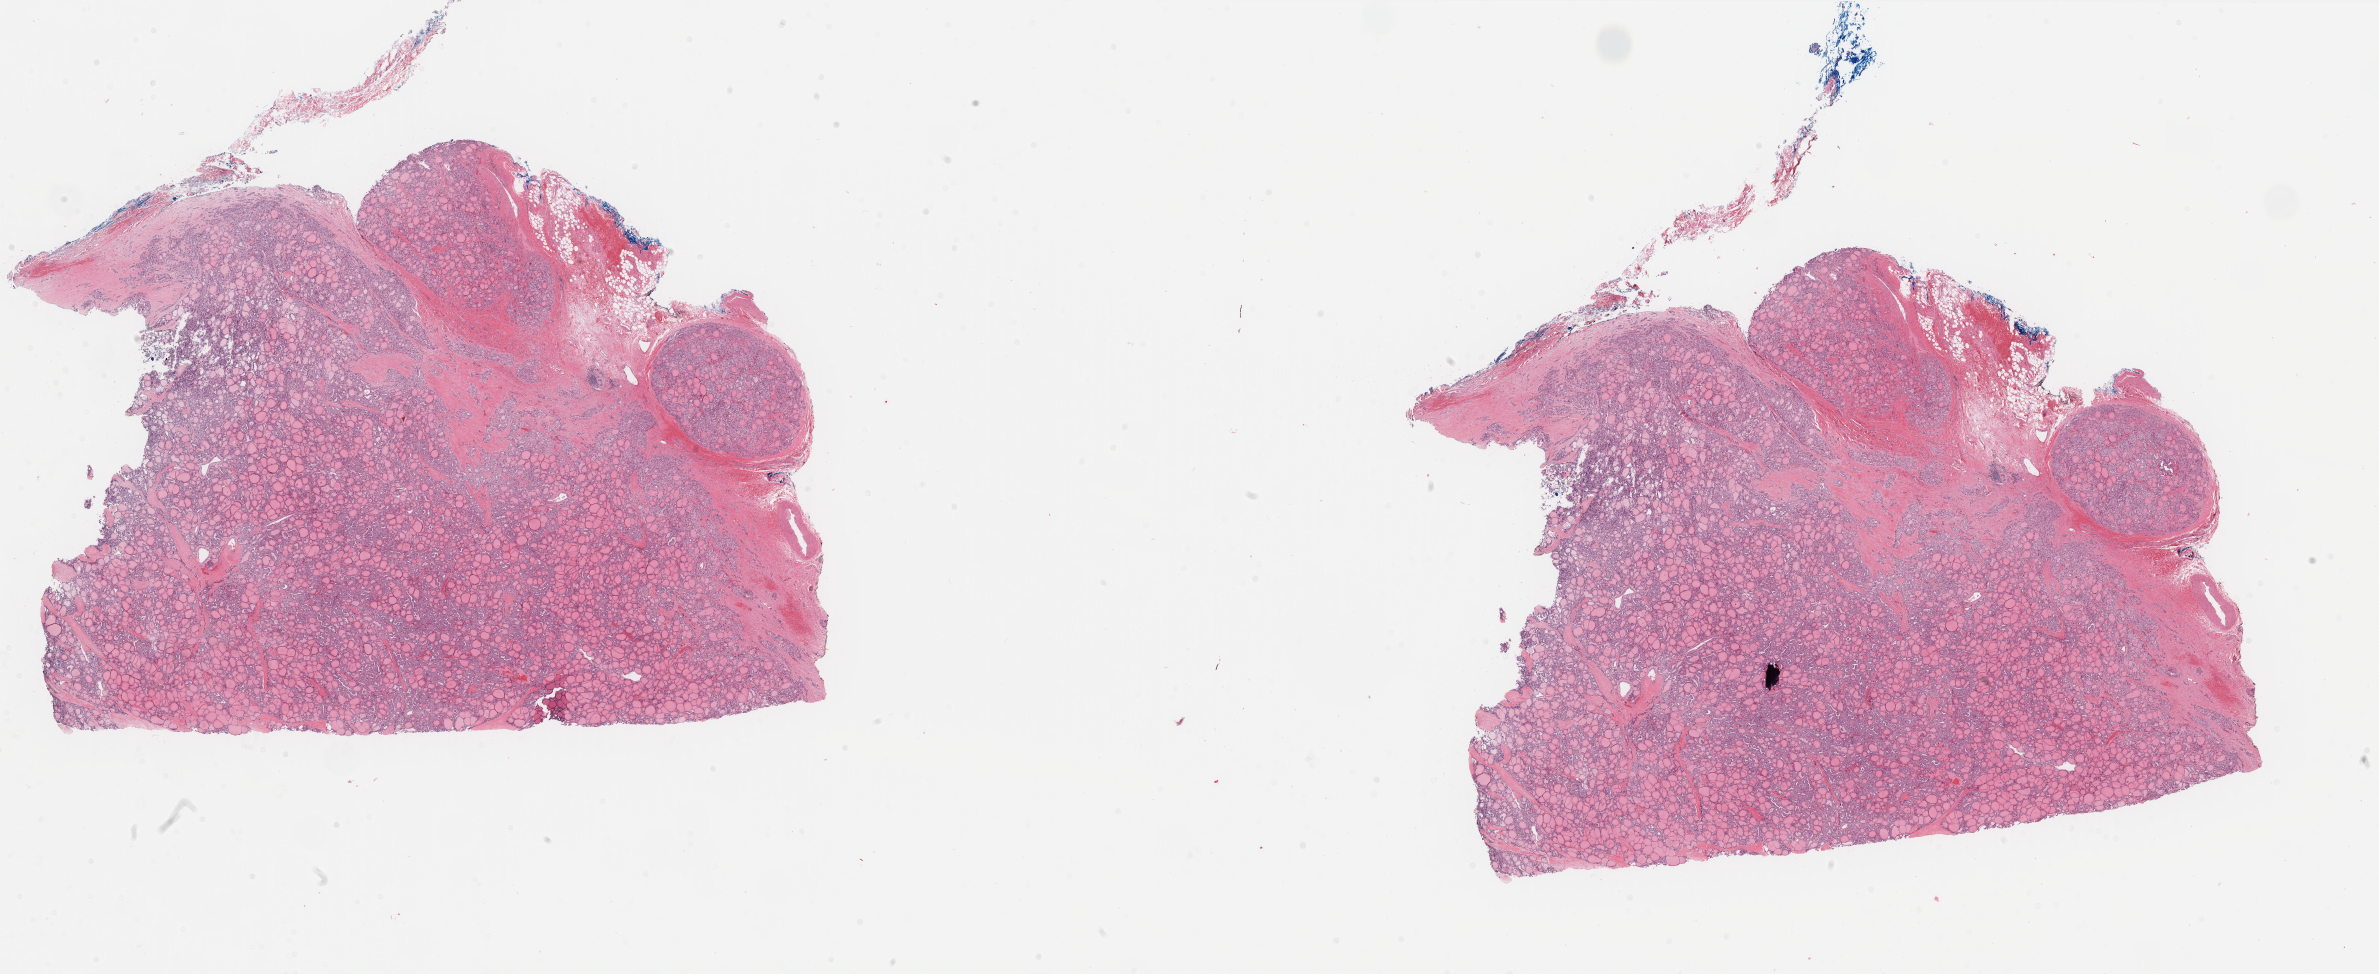
Digitized Hematoxylin and eosin (H&E) stained tissue section (whole slide) — a low-resolution overview of the entire scanned area, about 37.7 x 15.4 mm, formalin-fixed paraffin-embedded (FFPE) diagnostic section, sample: primary tumour, thyroid. Female, age 49 years at initial diagnosis.
* histologic diagnosis: Papillary adenocarcinoma, NOS
* lymph nodes positive (case pathology): 5 of 9 examined
* AJCC pathologic stage: IVA (7th edition)